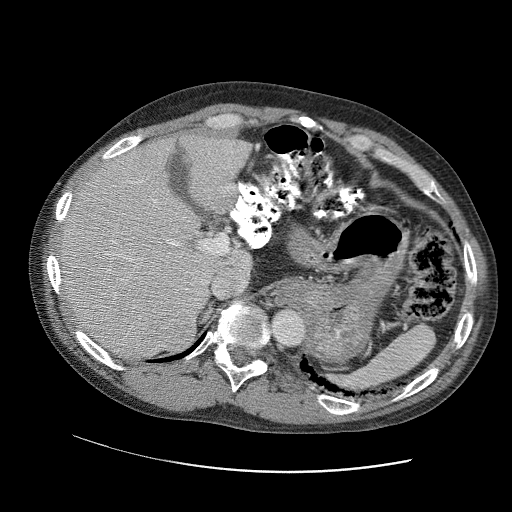
Contrast-enhanced abdominal CT (liver protocol), one axial slice; slice 71 of 109 in the series (ordered by position); reconstruction kernel STANDARD; 120 kVp; soft-tissue window (W 400 / L 40 HU); 512 × 512 image matrix. From the clinical record (not read from this slice): diagnosis: hepatocellular carcinoma (patient treated with transarterial chemoembolisation; whether this scan precedes or follows treatment is not stated here); TNM stage (as recorded): Stage-IIIC; Child-Pugh class: B; tumour differentiation: well differentiated; tumour nodularity: uninodular.
Annotated regions visible in this slice (semi-automatically segmented with operator editing):
- liver parenchyma outside the tumour (the mass and vessels are separate outlines, so this box may not span the whole liver): box from (x=58, y=128) to (x=252, y=362) px
- mass: (x=157, y=316)–(x=195, y=352)
- liver vessels: (x=71, y=151)–(x=248, y=331)